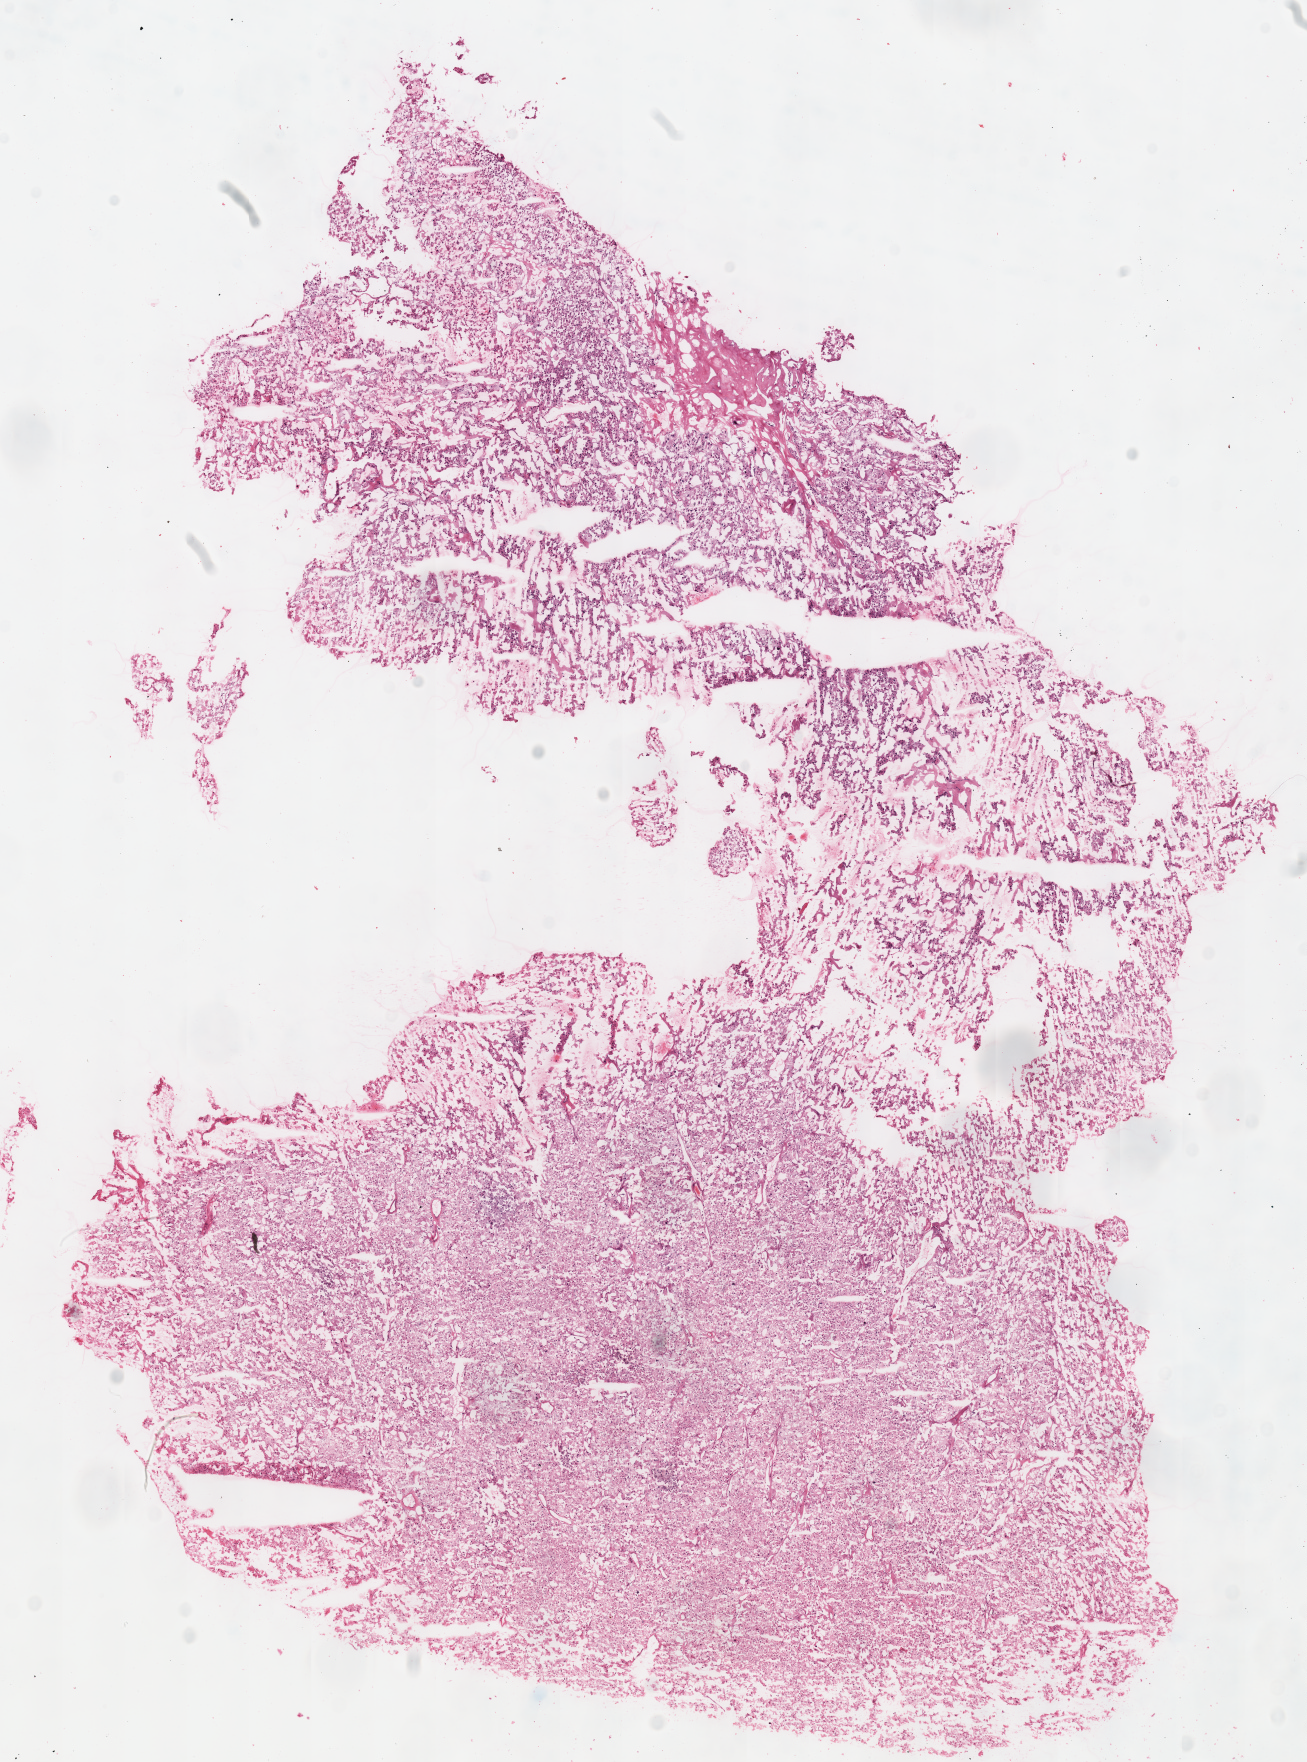
H&E-stained whole-slide image — low-resolution overview of the scanned area, about 10.3 x 13.9 mm (from a 40x scan); frozen section from the top of the tissue portion; primary tumour sample from the kidney. Patient: female, age at initial diagnosis 42 years. Composition of this section per pathologist review: tumour cells 100%, tumour nuclei 90%.
Diagnosis: Renal cell carcinoma, chromophobe type.